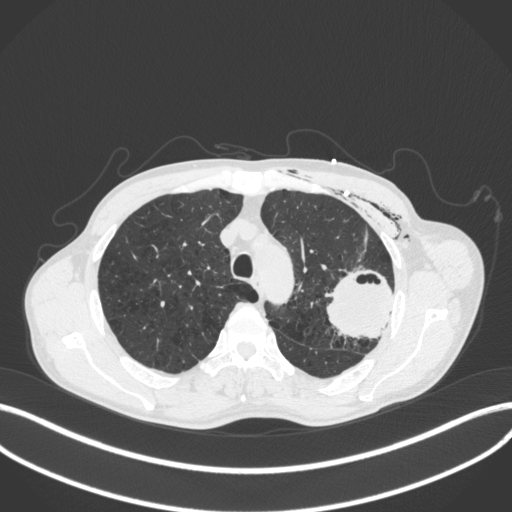
Chest CT, one axial slice; slice 307 of 416 in the series (ordered by position); reconstruction kernel B31f; 120 kVp; lung window (W 1500 / L -600 HU); 1 mm slice thickness; 512 × 512 image matrix, field of view 400 × 400 mm. Male patient, age 58 years. Case-level facts recorded for this patient, not image findings: clinical TNM (as recorded): T3 N0 M0.
Outlined on this slice (rectangle marked by the reading radiologist):
- lung tumour (recorded histology: adenocarcinoma): bounding box (x1, y1, x2, y2) in pixels: (326, 266, 403, 343)